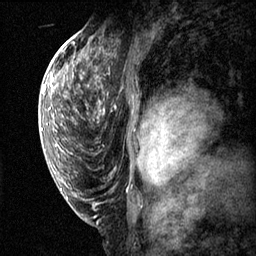
Breast MRI (dynamic contrast-enhanced), one sagittal slice; slice 39 of 60 in the series (ordered by position); dynamic contrast-enhanced series, image 2 of 3 at this slice position (ordered by acquisition); 1.5 T; TE 4.2 ms, TR 11.1 ms; 2 mm slice thickness; 256 × 256 image matrix, field of view 180 × 180 mm. Patient: female, 50 years.
Structures marked on this image (semi-automatically segmented with operator editing):
- analysis volume of interest (the breast-tissue region the enhancement analysis was run in; not a lesion): bounding box (x1, y1, x2, y2) in pixels: (82, 56, 161, 143)
- tumour enhancement mask (voxels above the 70 % enhancement threshold inside the analysis volume of interest): (141, 124, 159, 143)